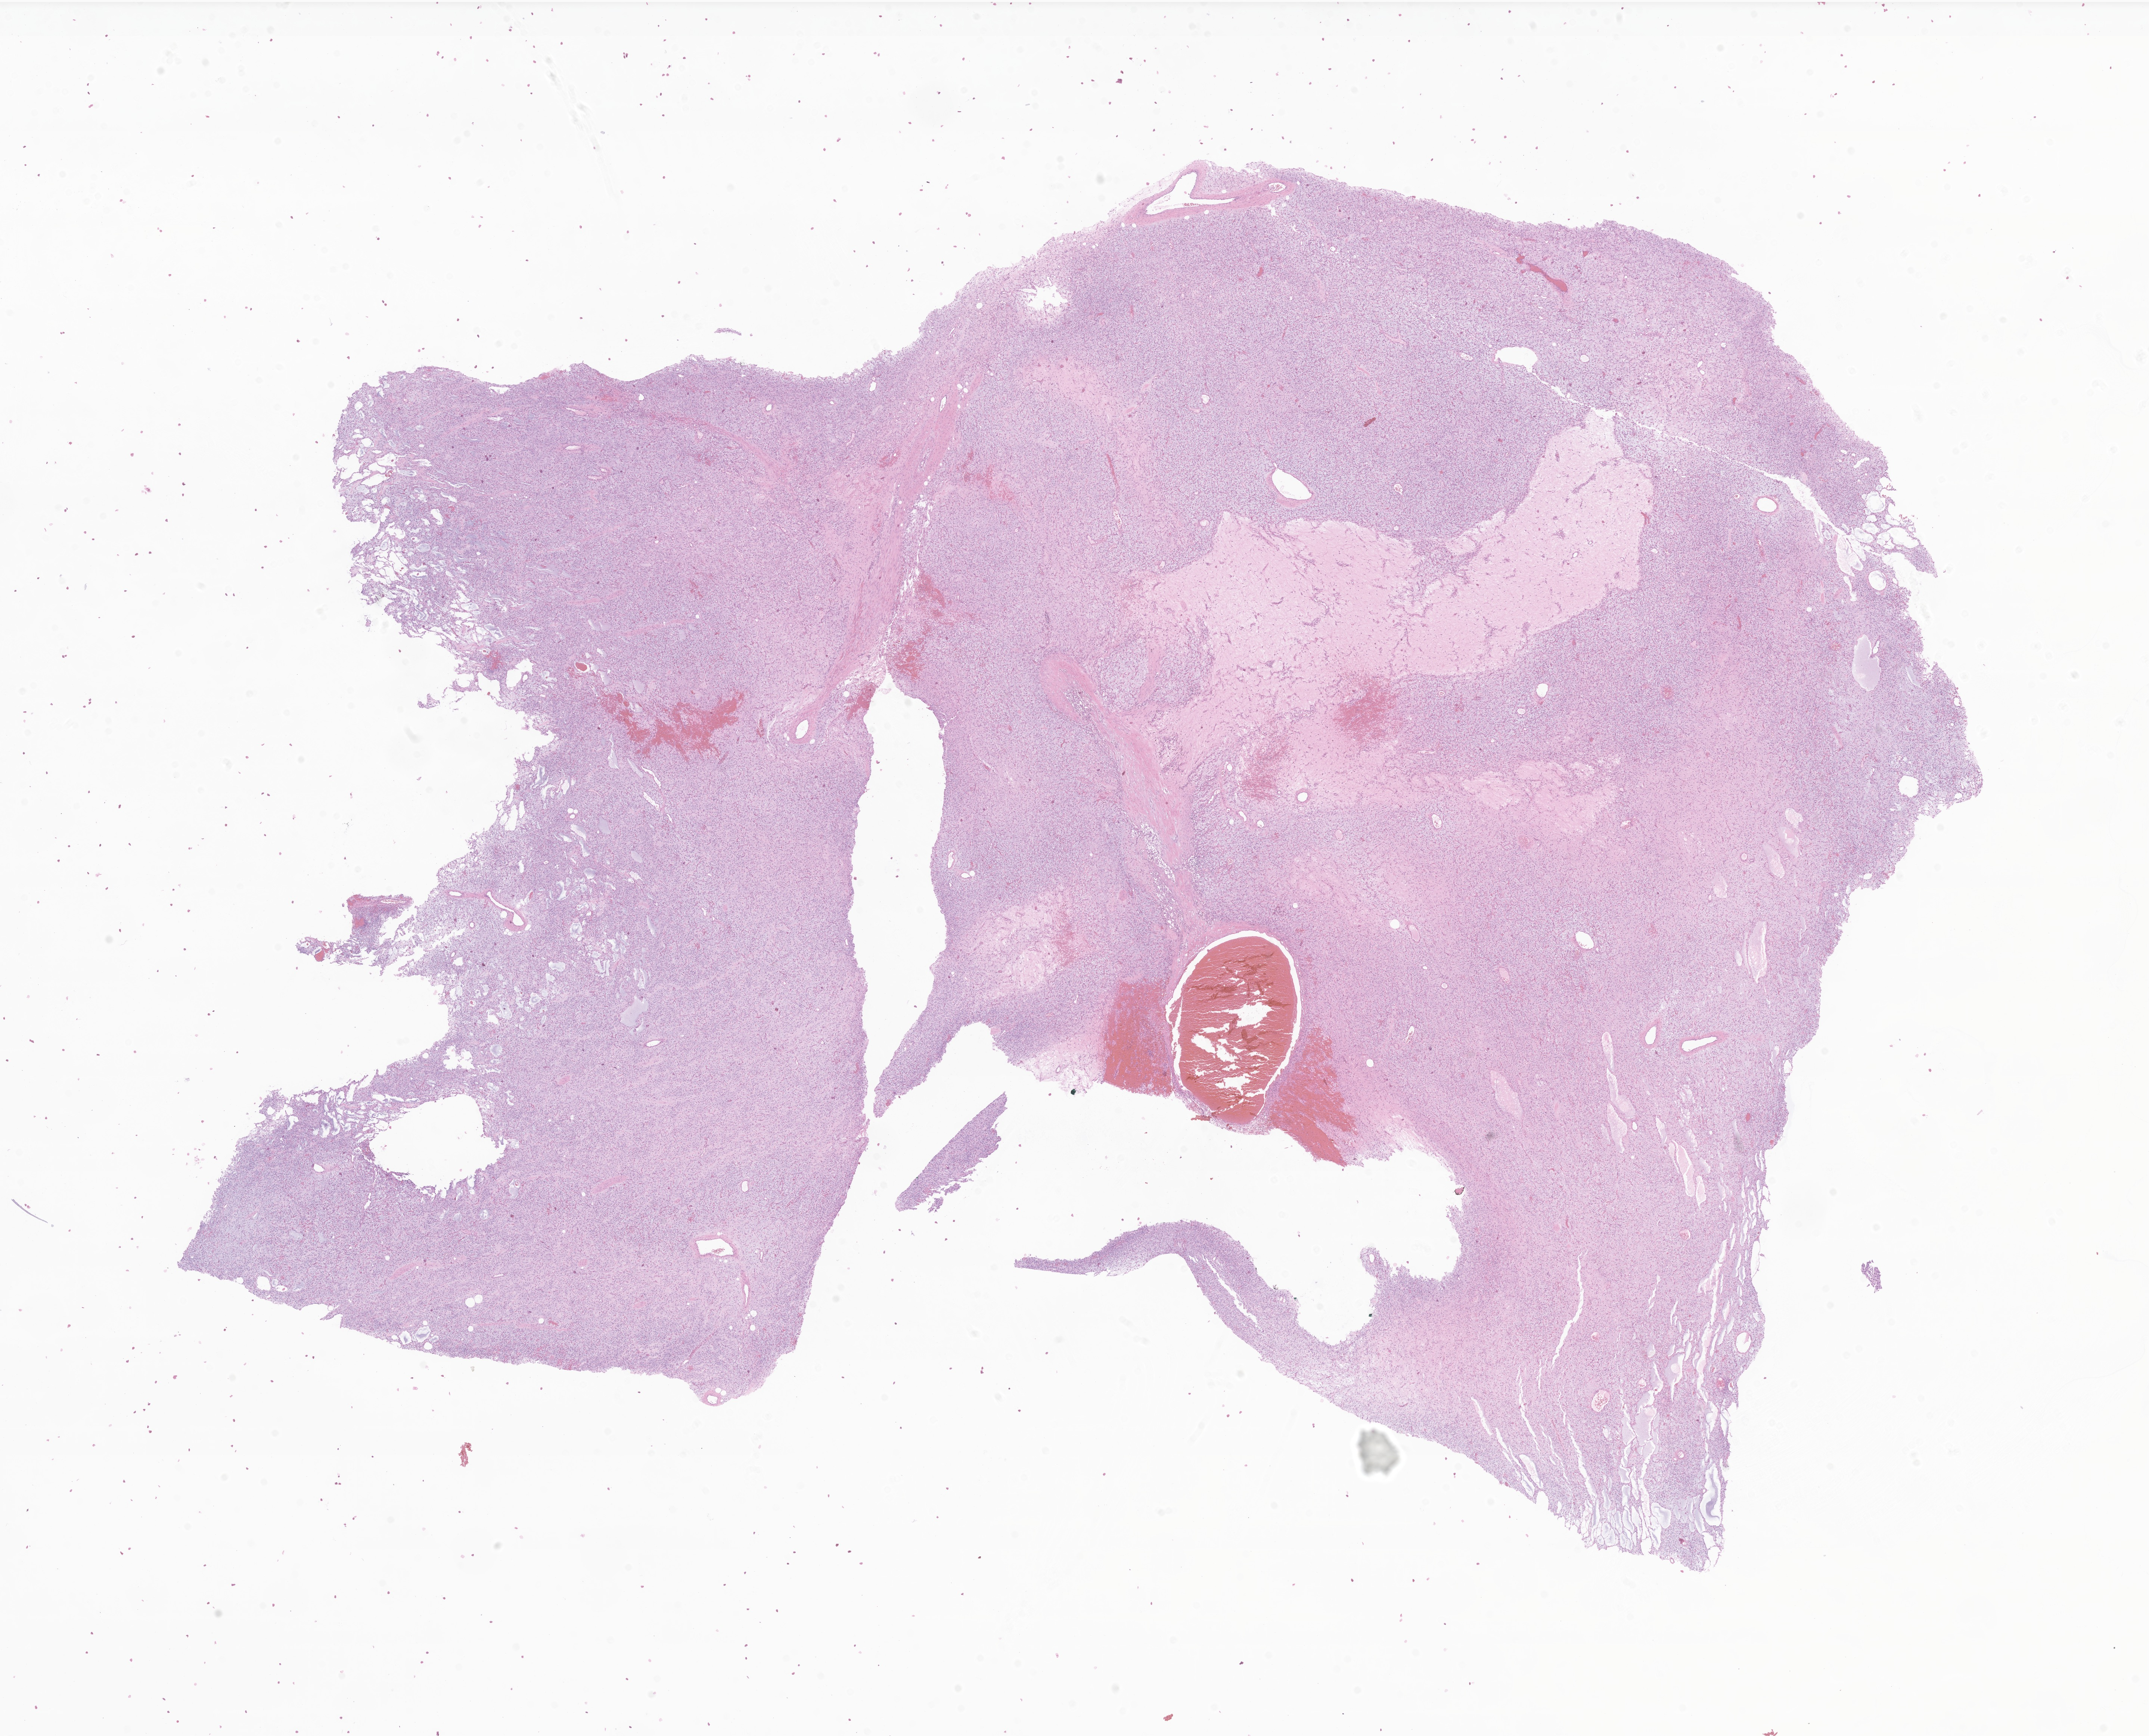
Whole-slide image, H&E stain of tumor tissue from the soft tissue — shown as a low-resolution overview of the whole scanned area (about 24.3 x 19.6 mm). FFPE section. Patient: male, age 176 months.
* recorded diagnosis: Liposarcoma, NOS